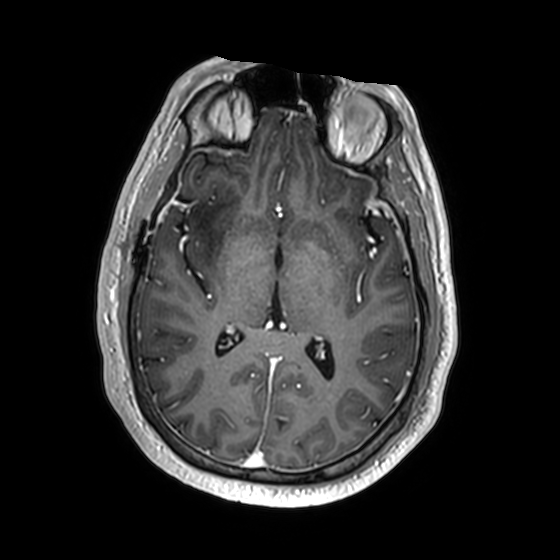
Brain MRI from a brain-tumour surgery series, one axial slice. Slice 91 of 174 in the series (ordered by position). T1-weighted post-contrast. 560 × 560 image matrix. Case-level facts recorded for this patient, not image findings: histopathology: Astrocytoma; WHO grade: 2; IDH mutation: yes; tumour location: Right Insular.
Annotated regions visible in this slice (expert manual segmentation):
- previous resection cavity: bounding box <178,197,188,202> (left, top, right, bottom; pixels)